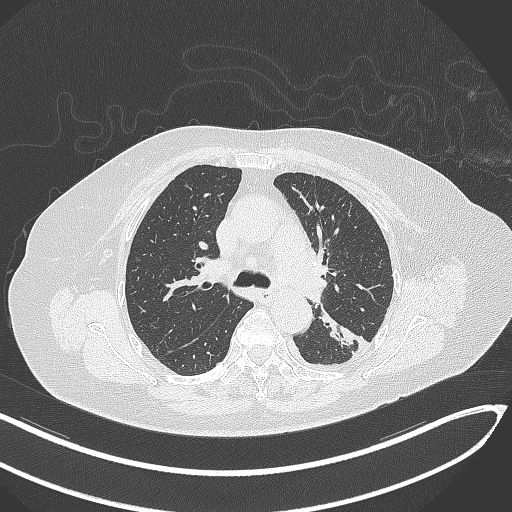
Chest CT, one axial slice; slice 206 of 270 in the series (ordered by position); 120 kVp; lung window (W 1500 / L -600 HU); 1 mm slice thickness; 512 × 512 image matrix, field of view 400 × 400 mm. Female patient, age 76 years. From the clinical record (not read from this slice): clinical TNM (as recorded): T1c N0 M0.
Annotated regions visible in this slice (rectangle marked by the reading radiologist):
- lung tumour (recorded histology: adenocarcinoma): bounding box <317,307,362,353> (left, top, right, bottom; pixels)